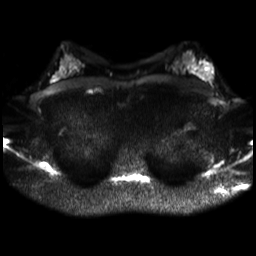
Breast MRI, one axial slice; diffusion-weighted series; image 2 of 4 stored at this slice position (different b-values; order by instance number); 3 T; 4 mm slice thickness; 256 × 256 image matrix, field of view 320 × 320 mm. Female patient.
Outlined on this slice (outlined manually by an expert reader):
- tumour on diffusion-weighted imaging: bounding box (x1, y1, x2, y2) in pixels: (202, 69, 212, 78)